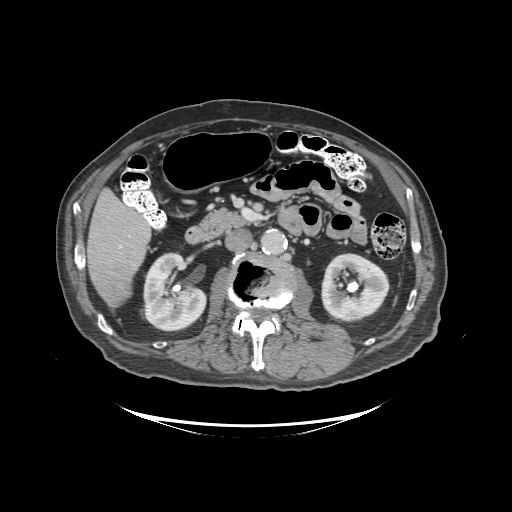
Contrast-enhanced abdominal CT (liver protocol), one axial slice; slice 39 of 99 in the series (ordered by position); reconstruction kernel STANDARD; soft-tissue window (W 400 / L 40 HU); 2.5 mm slice thickness; 512 × 512 image matrix. Case-level facts recorded for this patient, not image findings: diagnosis: hepatocellular carcinoma (patient treated with transarterial chemoembolisation; whether this scan precedes or follows treatment is not stated here); TNM stage (as recorded): Stage-I; Child-Pugh class: A; tumour differentiation: moderately differentiated; tumour nodularity: uninodular.
Outlined on this slice (semi-automatically segmented with operator editing):
- liver parenchyma outside the tumour (the mass and vessels are separate outlines, so this box may not span the whole liver): bounding box <86,188,150,308> (left, top, right, bottom; pixels)
- mass: <93,262,130,303>
- liver vessels: <119,246,122,248>